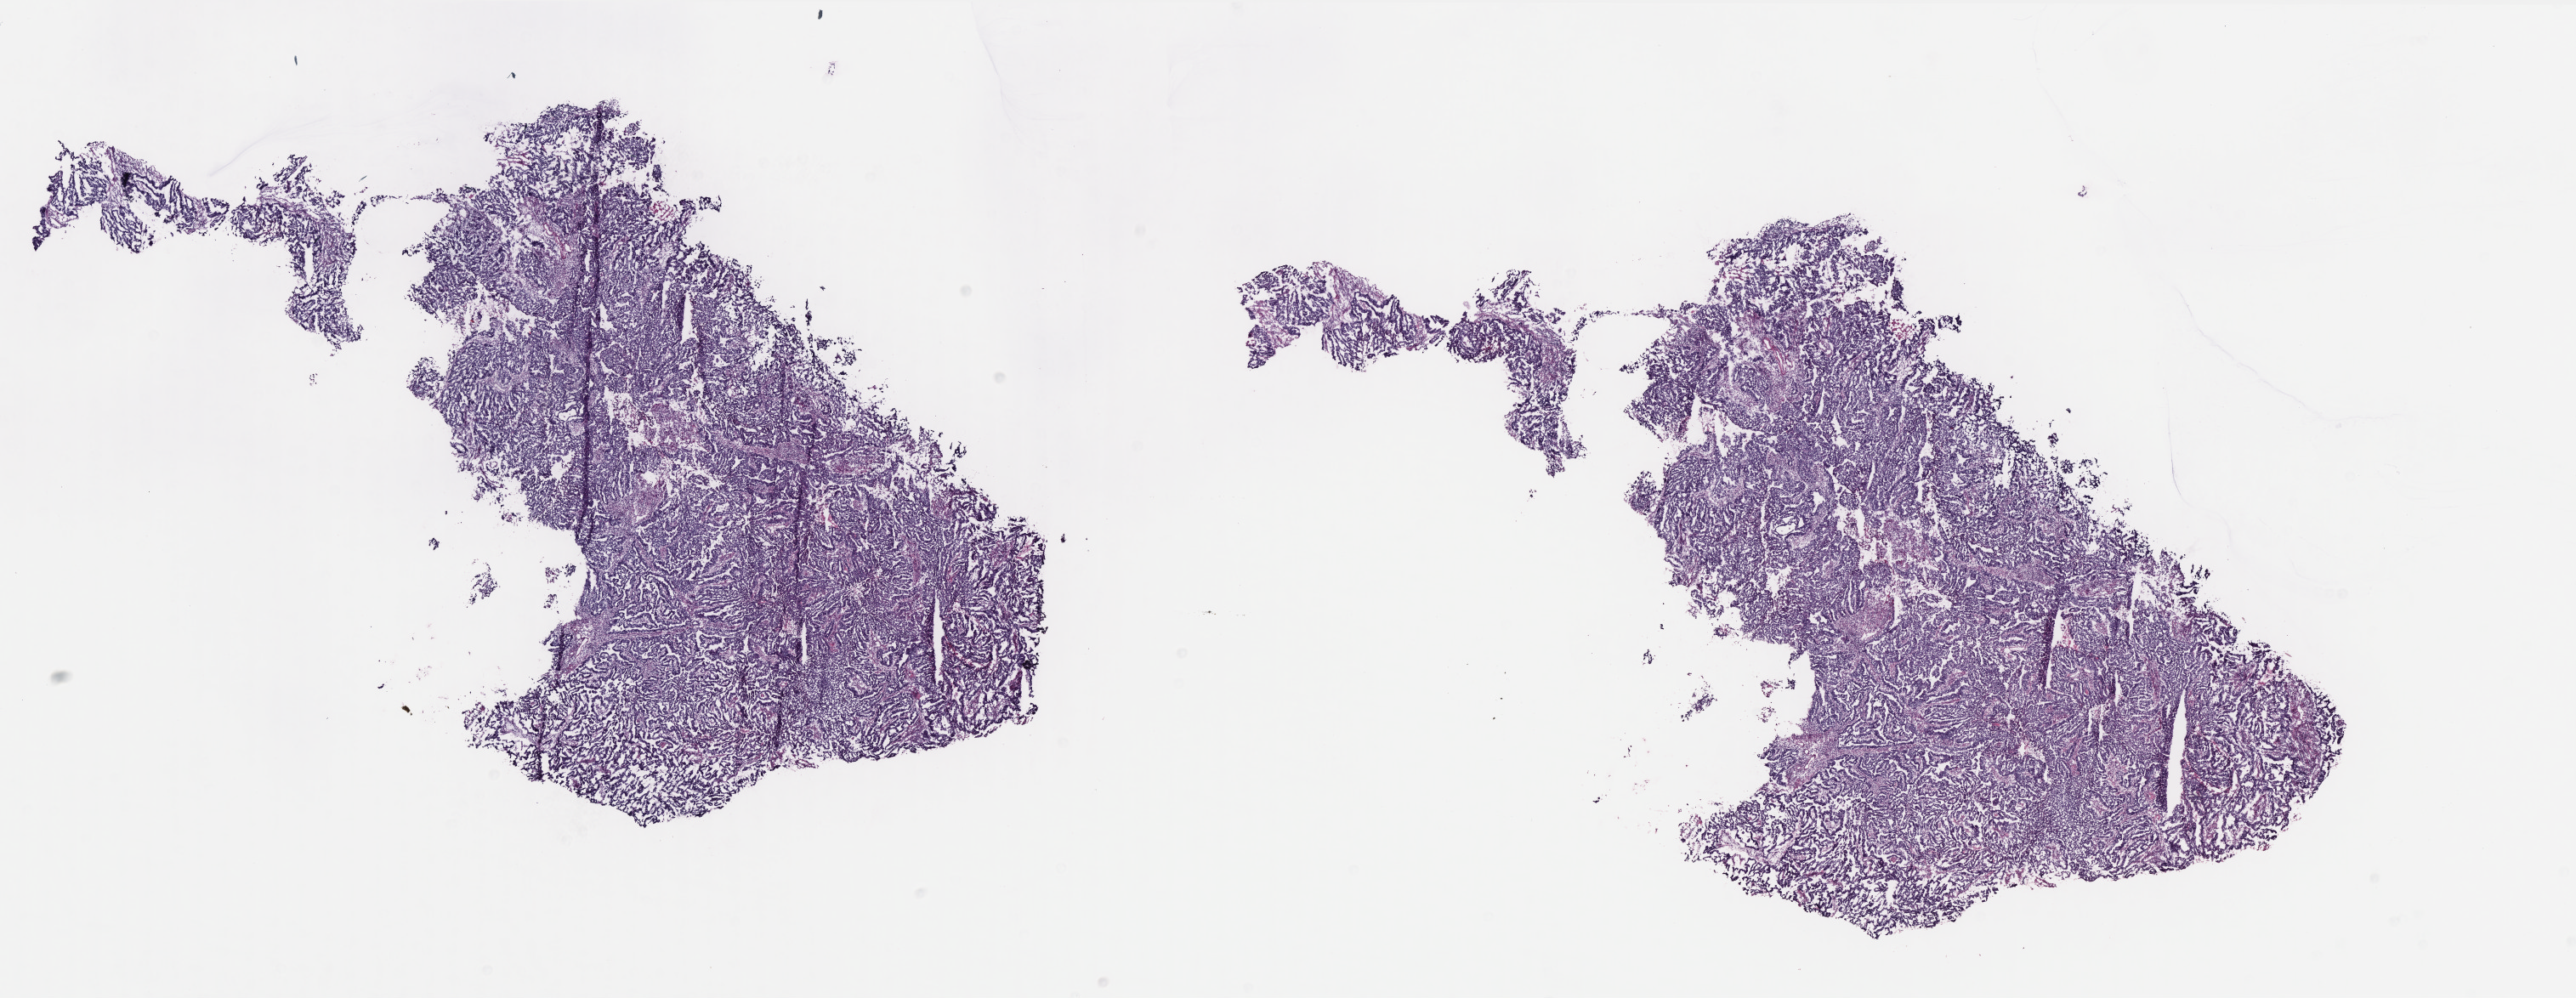
H&E-stained whole-slide image, low-resolution overview of the scanned area, about 24.3 x 9.4 mm. Frozen section from the top of the tissue portion. Uterus, primary tumour sample. Female patient; age at initial diagnosis 57 years. Histologic grade: G3 (poorly differentiated). Slide review estimates, as recorded: tumour cells 80%, tumour nuclei 90%, normal cells 10%, stromal cells 0%, necrosis 10%. Inflammatory infiltration, as recorded: lymphocyte infiltration 20%, monocyte infiltration 0%, neutrophil infiltration 10%.
Diagnosis: Endometrioid adenocarcinoma, NOS (endometrium). FIGO stage: IA.